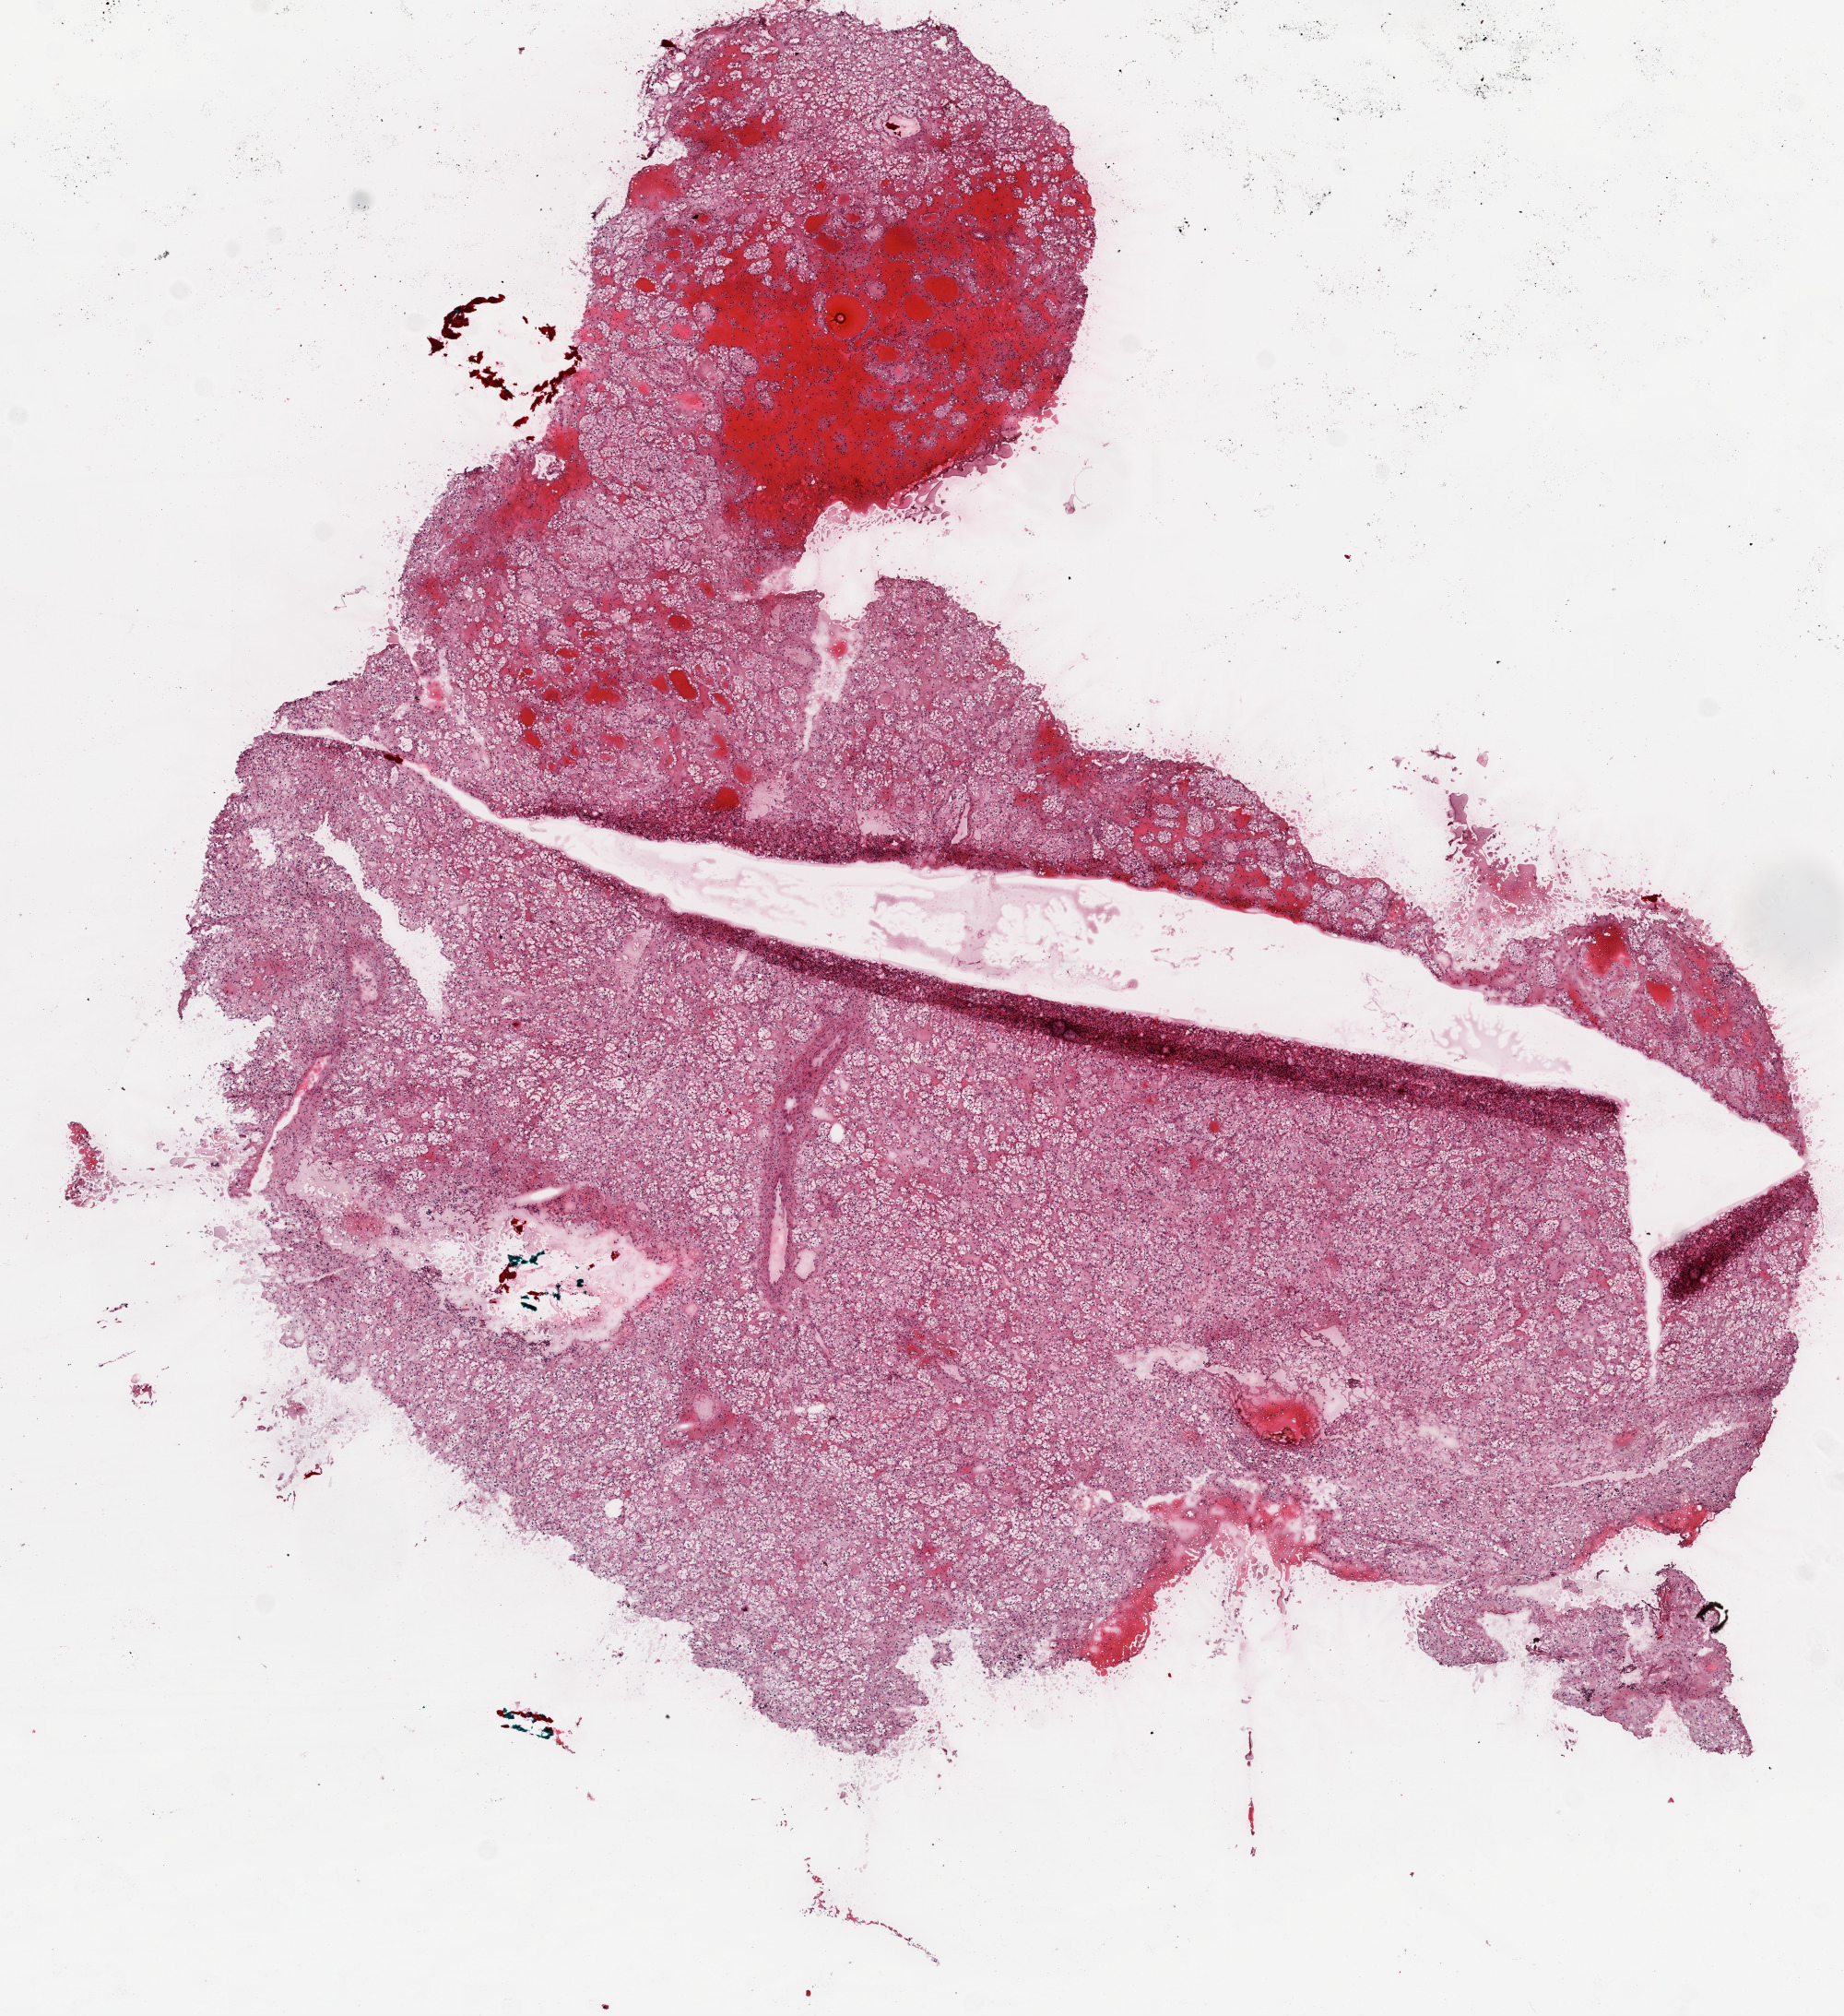
Whole-slide histology image, H&E-stained — a low-resolution overview of the entire scanned area, about 8.0 x 8.8 mm (acquisition: 20x scan); frozen section from the top of the tissue portion; sample: primary tumour, kidney. Patient: male, age at initial diagnosis 54 years. Histologic grade: G3 (poorly differentiated). Composition of this section per pathologist review: tumour cells 95%, tumour nuclei 90%, normal cells 0%, stromal cells 5%, necrosis 0%.
AJCC pathologic stage: I. Histologic diagnosis: Clear cell adenocarcinoma, NOS. Laterality: left.